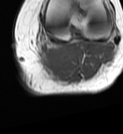
MRI of an extremity soft-tissue mass, one axial slice; MR volume resampled by the dataset authors to the PET/CT grid (not the native acquisition matrix); 3.27 mm slice thickness; 123 × 134 image matrix, field of view 120 × 131 mm. Female patient. From the clinical record (not read from this slice): histological type: extraskeletal high grade osteogenic sarcoma; grade: high; site of the primary tumour: left calf.
Structures marked on this image (expert contour drawn on MRI and transferred to this co-registered scan by the dataset authors):
- gross tumour volume (mass): bounding box (x1, y1, x2, y2) in pixels: (40, 45, 73, 72)